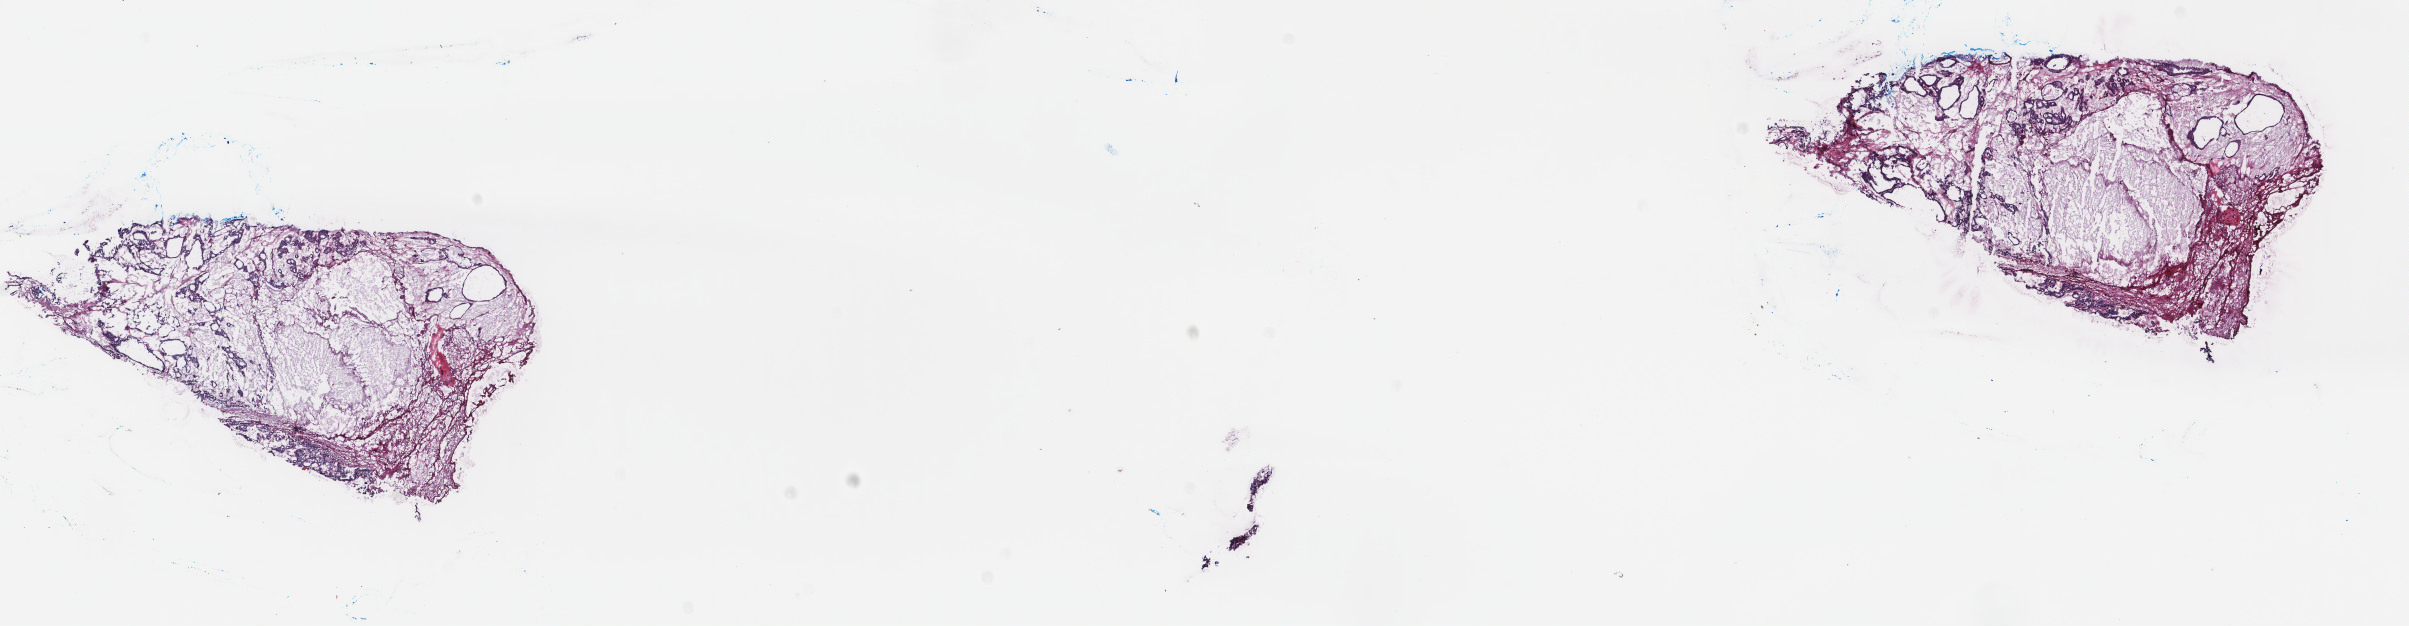
Whole-slide histology image, H&E-stained, shown as a low-resolution overview of the whole scanned area (about 19.1 x 5.0 mm, acquisition: 40x scan); frozen section from the top of the tissue portion; thyroid, primary tumour sample. Patient: female, age at initial diagnosis 52 years. Composition of this section per pathologist review: tumour cells 30%, tumour nuclei 100%, normal cells 0%, stromal cells 70%, necrosis 0%. Infiltration values recorded for this section: lymphocyte infiltration 0%, monocyte infiltration 2%, neutrophil infiltration 6%.
Laterality: right. AJCC pathologic stage: I (7th edition). TNM: T1a NX MX. Diagnosis: Papillary carcinoma, follicular variant.